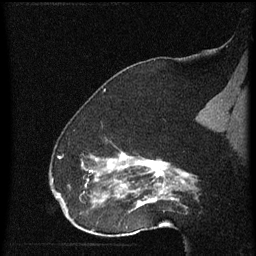
Breast MRI (dynamic contrast-enhanced), one sagittal slice. Position 40 of 60 along the scan axis. Dynamic contrast-enhanced series, image 2 of 4 at this slice position (ordered by acquisition). 1.5 T. TE 4.2 ms, TR 8 ms. 256 × 256 image matrix. Patient: female, 52 years.
Outlined on this slice (semi-automatically segmented with operator editing):
- analysis volume of interest (the breast-tissue region the enhancement analysis was run in; not a lesion): bounding box [x1, y1, x2, y2] px = [73, 148, 172, 219]
- tumour enhancement mask (voxels above the 70 % enhancement threshold inside the analysis volume of interest): [82, 154, 172, 207]